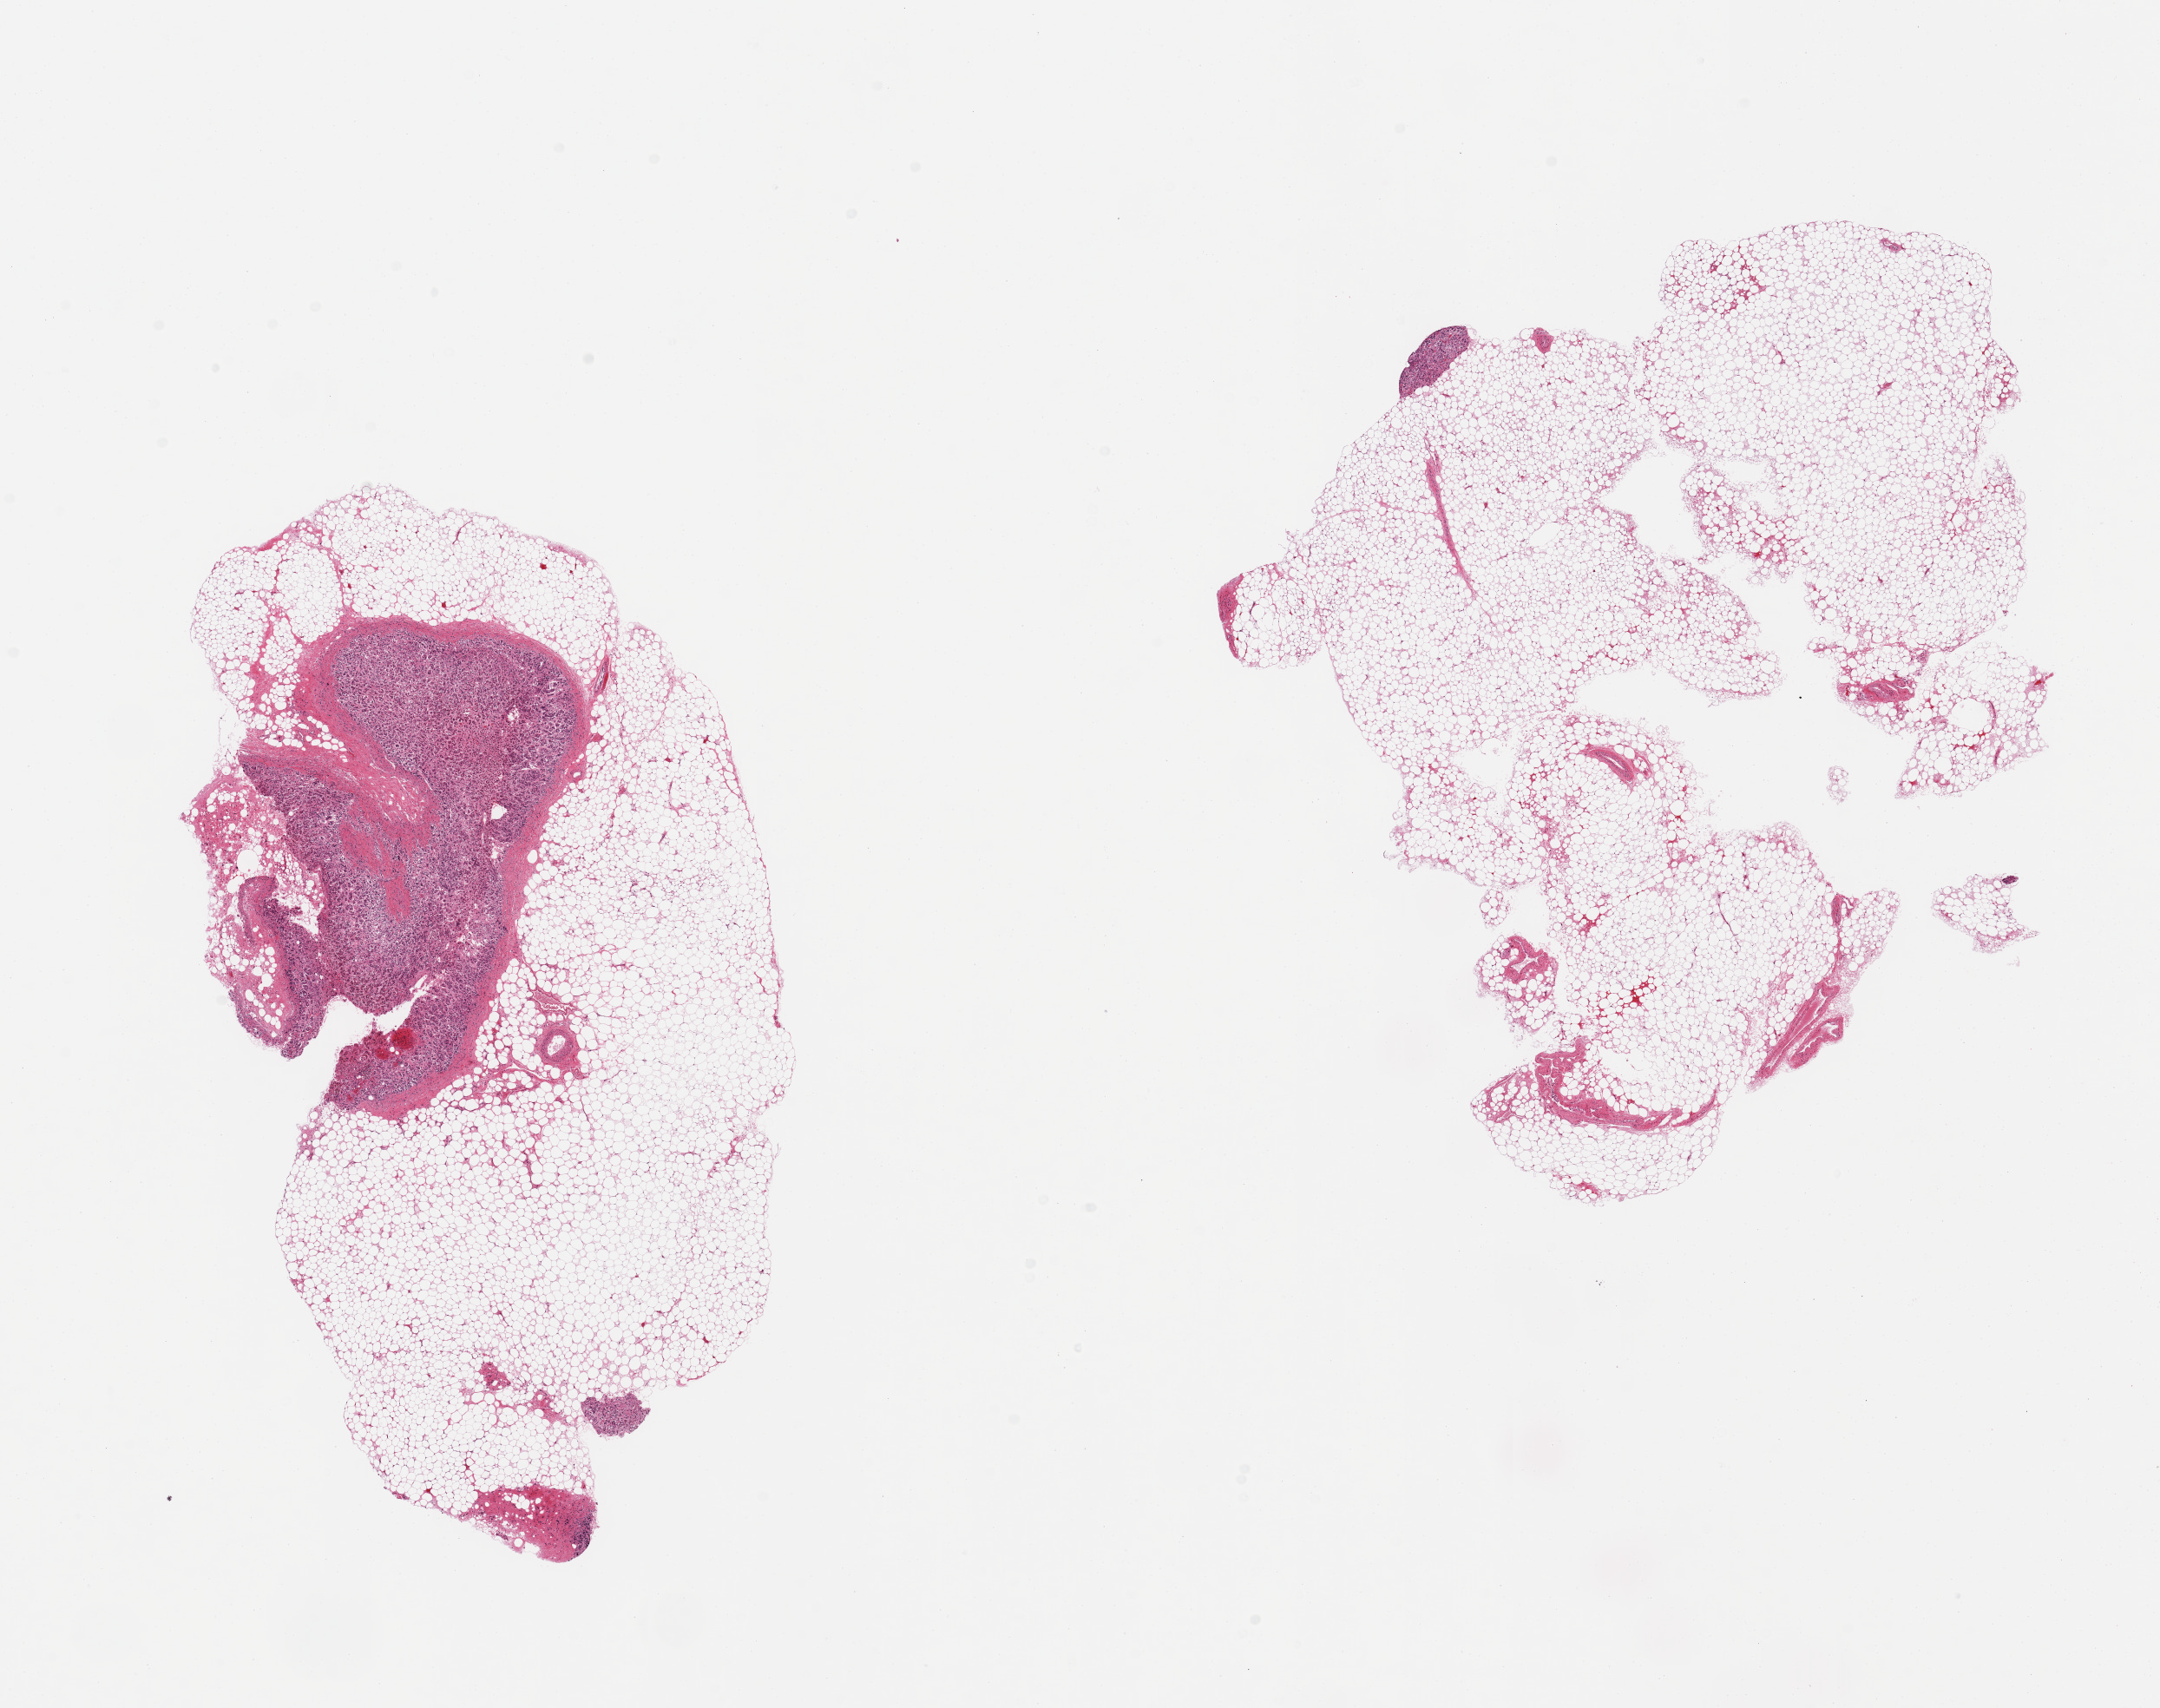
Whole-slide image, hematoxylin and eosin (H&E) stain, brightfield, whole scanned area (about 19.7 x 15.6 mm, acquisition: 20x scan) shown as a low-resolution overview, PAXgene-fixed paraffin-embedded (PFPE) section, target tissue: adrenal gland, tissue donor sample. Male donor.
Pathologist's review note for this sample: 2 pieces, focal cortex, ~25% of tissue, mainly peripheral fat.